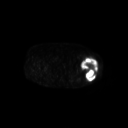
FDG PET of an extremity soft-tissue mass (from a PET/CT study), one axial slice. Position 237 of 267 along the scan axis. 128 × 128 image matrix. Patient: female, 62 years. From the clinical record (not read from this slice): histological type: undifferentiated – high grade; grade: high; site of the primary tumour: left thigh.
Outlined on this slice (expert contour drawn on MRI and transferred to this co-registered scan by the dataset authors):
- gross tumour volume including surrounding oedema: bounding box <81,57,98,81> (left, top, right, bottom; pixels)
- gross tumour volume (mass): <81,57,98,81>